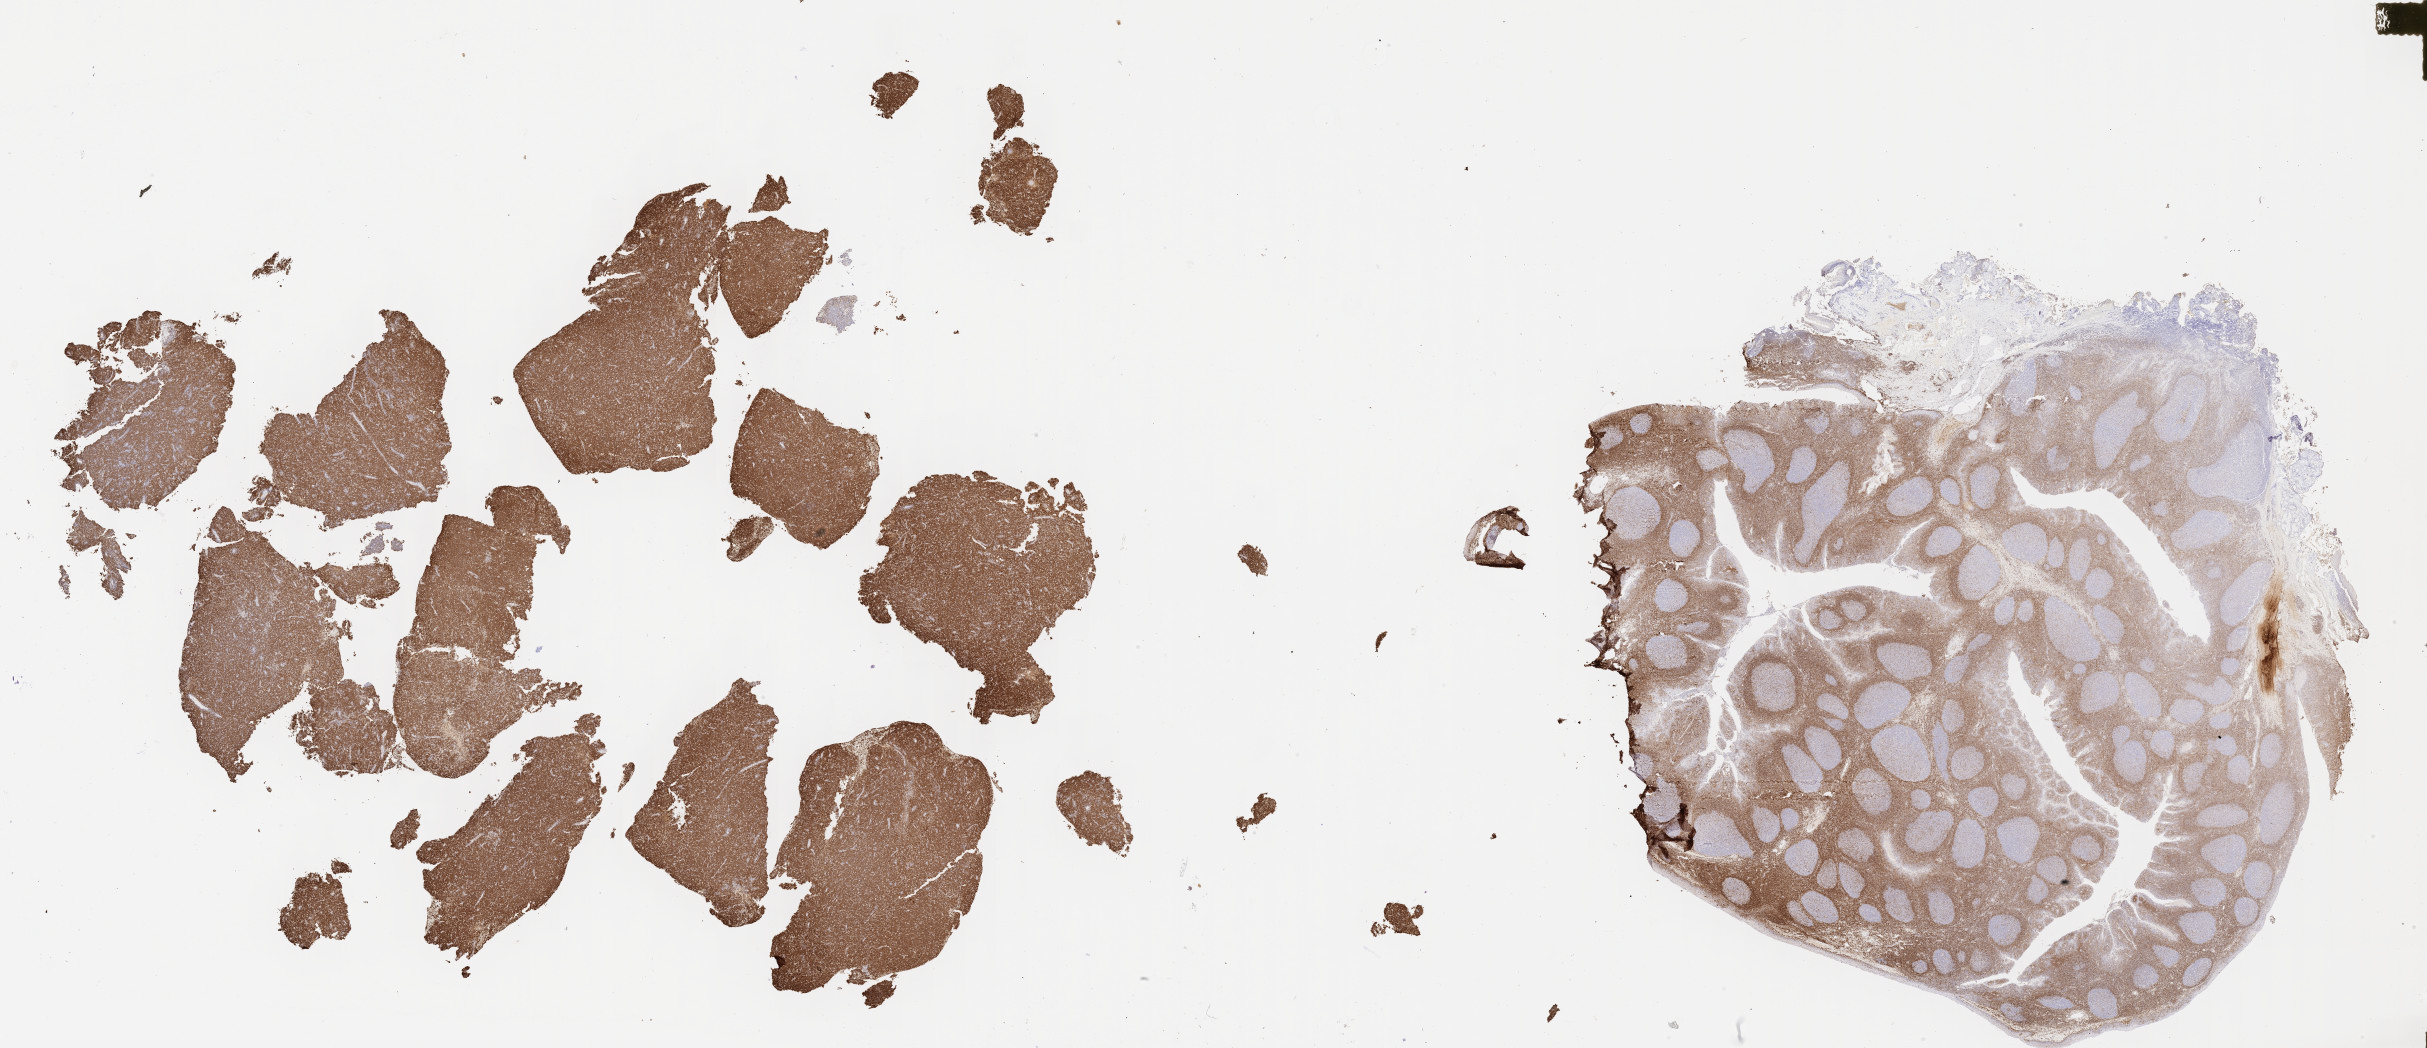
IHC for BCL2, whole-slide image — low-resolution overview of the scanned area, about 39.2 x 16.9 mm, specimen: tumor tissue, anatomic site: lymph node. Patient: female, aged 50.
Diagnosis: Diffuse large B-cell lymphoma, NOS.